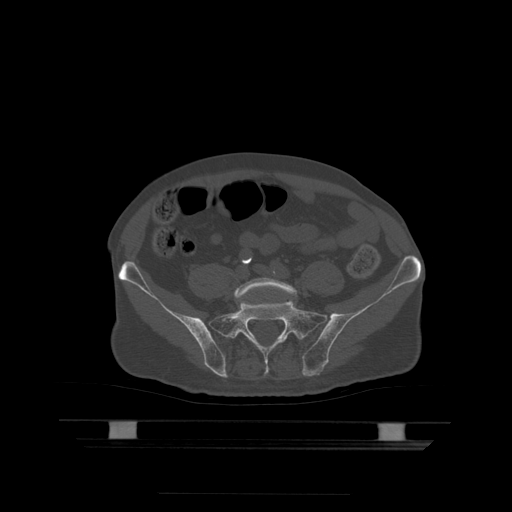
CT including the spine, one axial slice. Slice 58 of 522 in the series (ordered by position). Bone window (W 1800 / L 400 HU). 1.25 mm slice thickness. 512 × 512 image matrix. Patient age 68 years. Case-level facts recorded for this patient, not image findings: primary cancer: urothelial.
Outlined on this slice (semi-automatic segmentation, software-assisted and operator-edited):
- L5 vertebra: bounding box [x1, y1, x2, y2] px = [234, 278, 297, 302]